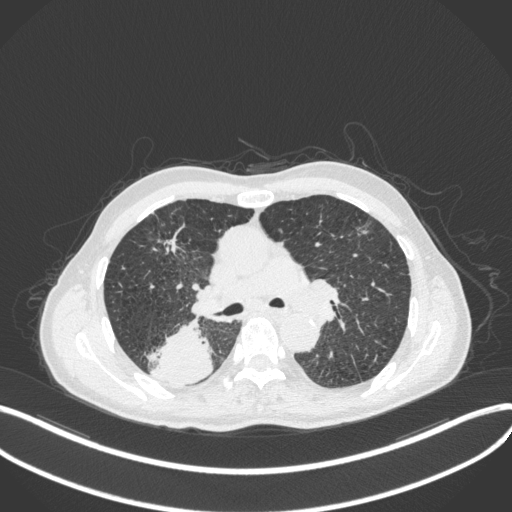
Chest CT, one axial slice; position 281 of 423 along the scan axis; reconstruction kernel B31f; lung window (W 1500 / L -600 HU); 1 mm slice thickness; 512 × 512 image matrix, field of view 400 × 400 mm. Patient: male, 79 years. Case-level facts recorded for this patient, not image findings: clinical TNM (as recorded): T3 N0 M0.
Outlined on this slice (rectangle marked by the reading radiologist):
- lung tumour (recorded histology: adenocarcinoma): bounding box [x1, y1, x2, y2] px = [144, 314, 216, 388]